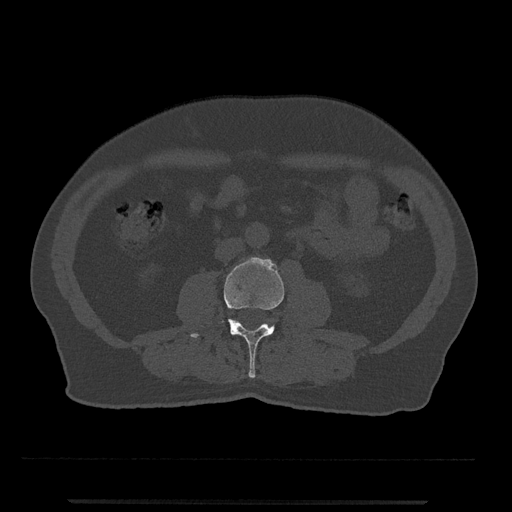
CT including the spine, one axial slice; position 194 of 797 along the scan axis; bone window (W 1800 / L 400 HU); 0.5 mm slice thickness; 512 × 512 image matrix, field of view 419 × 419 mm. Patient: male, 63 years. From the clinical record (not read from this slice): primary cancer: prostate.
Annotated regions visible in this slice (semi-automatically segmented with operator editing):
- L3 vertebra: bounding box [x1, y1, x2, y2] px = [190, 257, 284, 378]